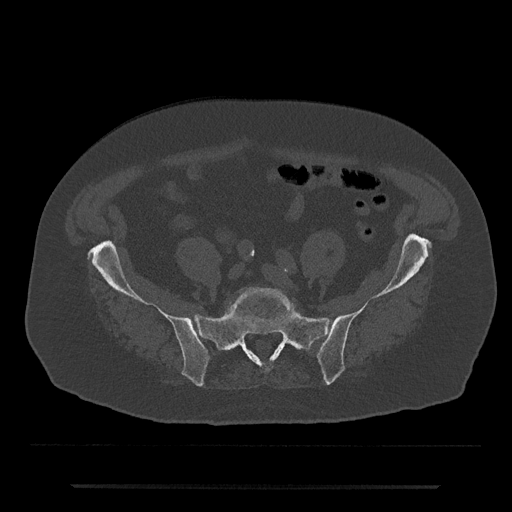
CT including the spine, one axial slice. Slice 247 of 797 in the series (ordered by position). 120 kVp. Bone window (W 1800 / L 400 HU). 0.5 mm slice thickness. 512 × 512 image matrix. Male patient, age 80 years. From the clinical record (not read from this slice): primary cancer: prostate; vertebrae with lytic lesions (as recorded): L1, T11.
Outlined on this slice (semi-automatic segmentation, software-assisted and operator-edited):
- L5 vertebra: bounding box (x1, y1, x2, y2) in pixels: (228, 287, 299, 318)